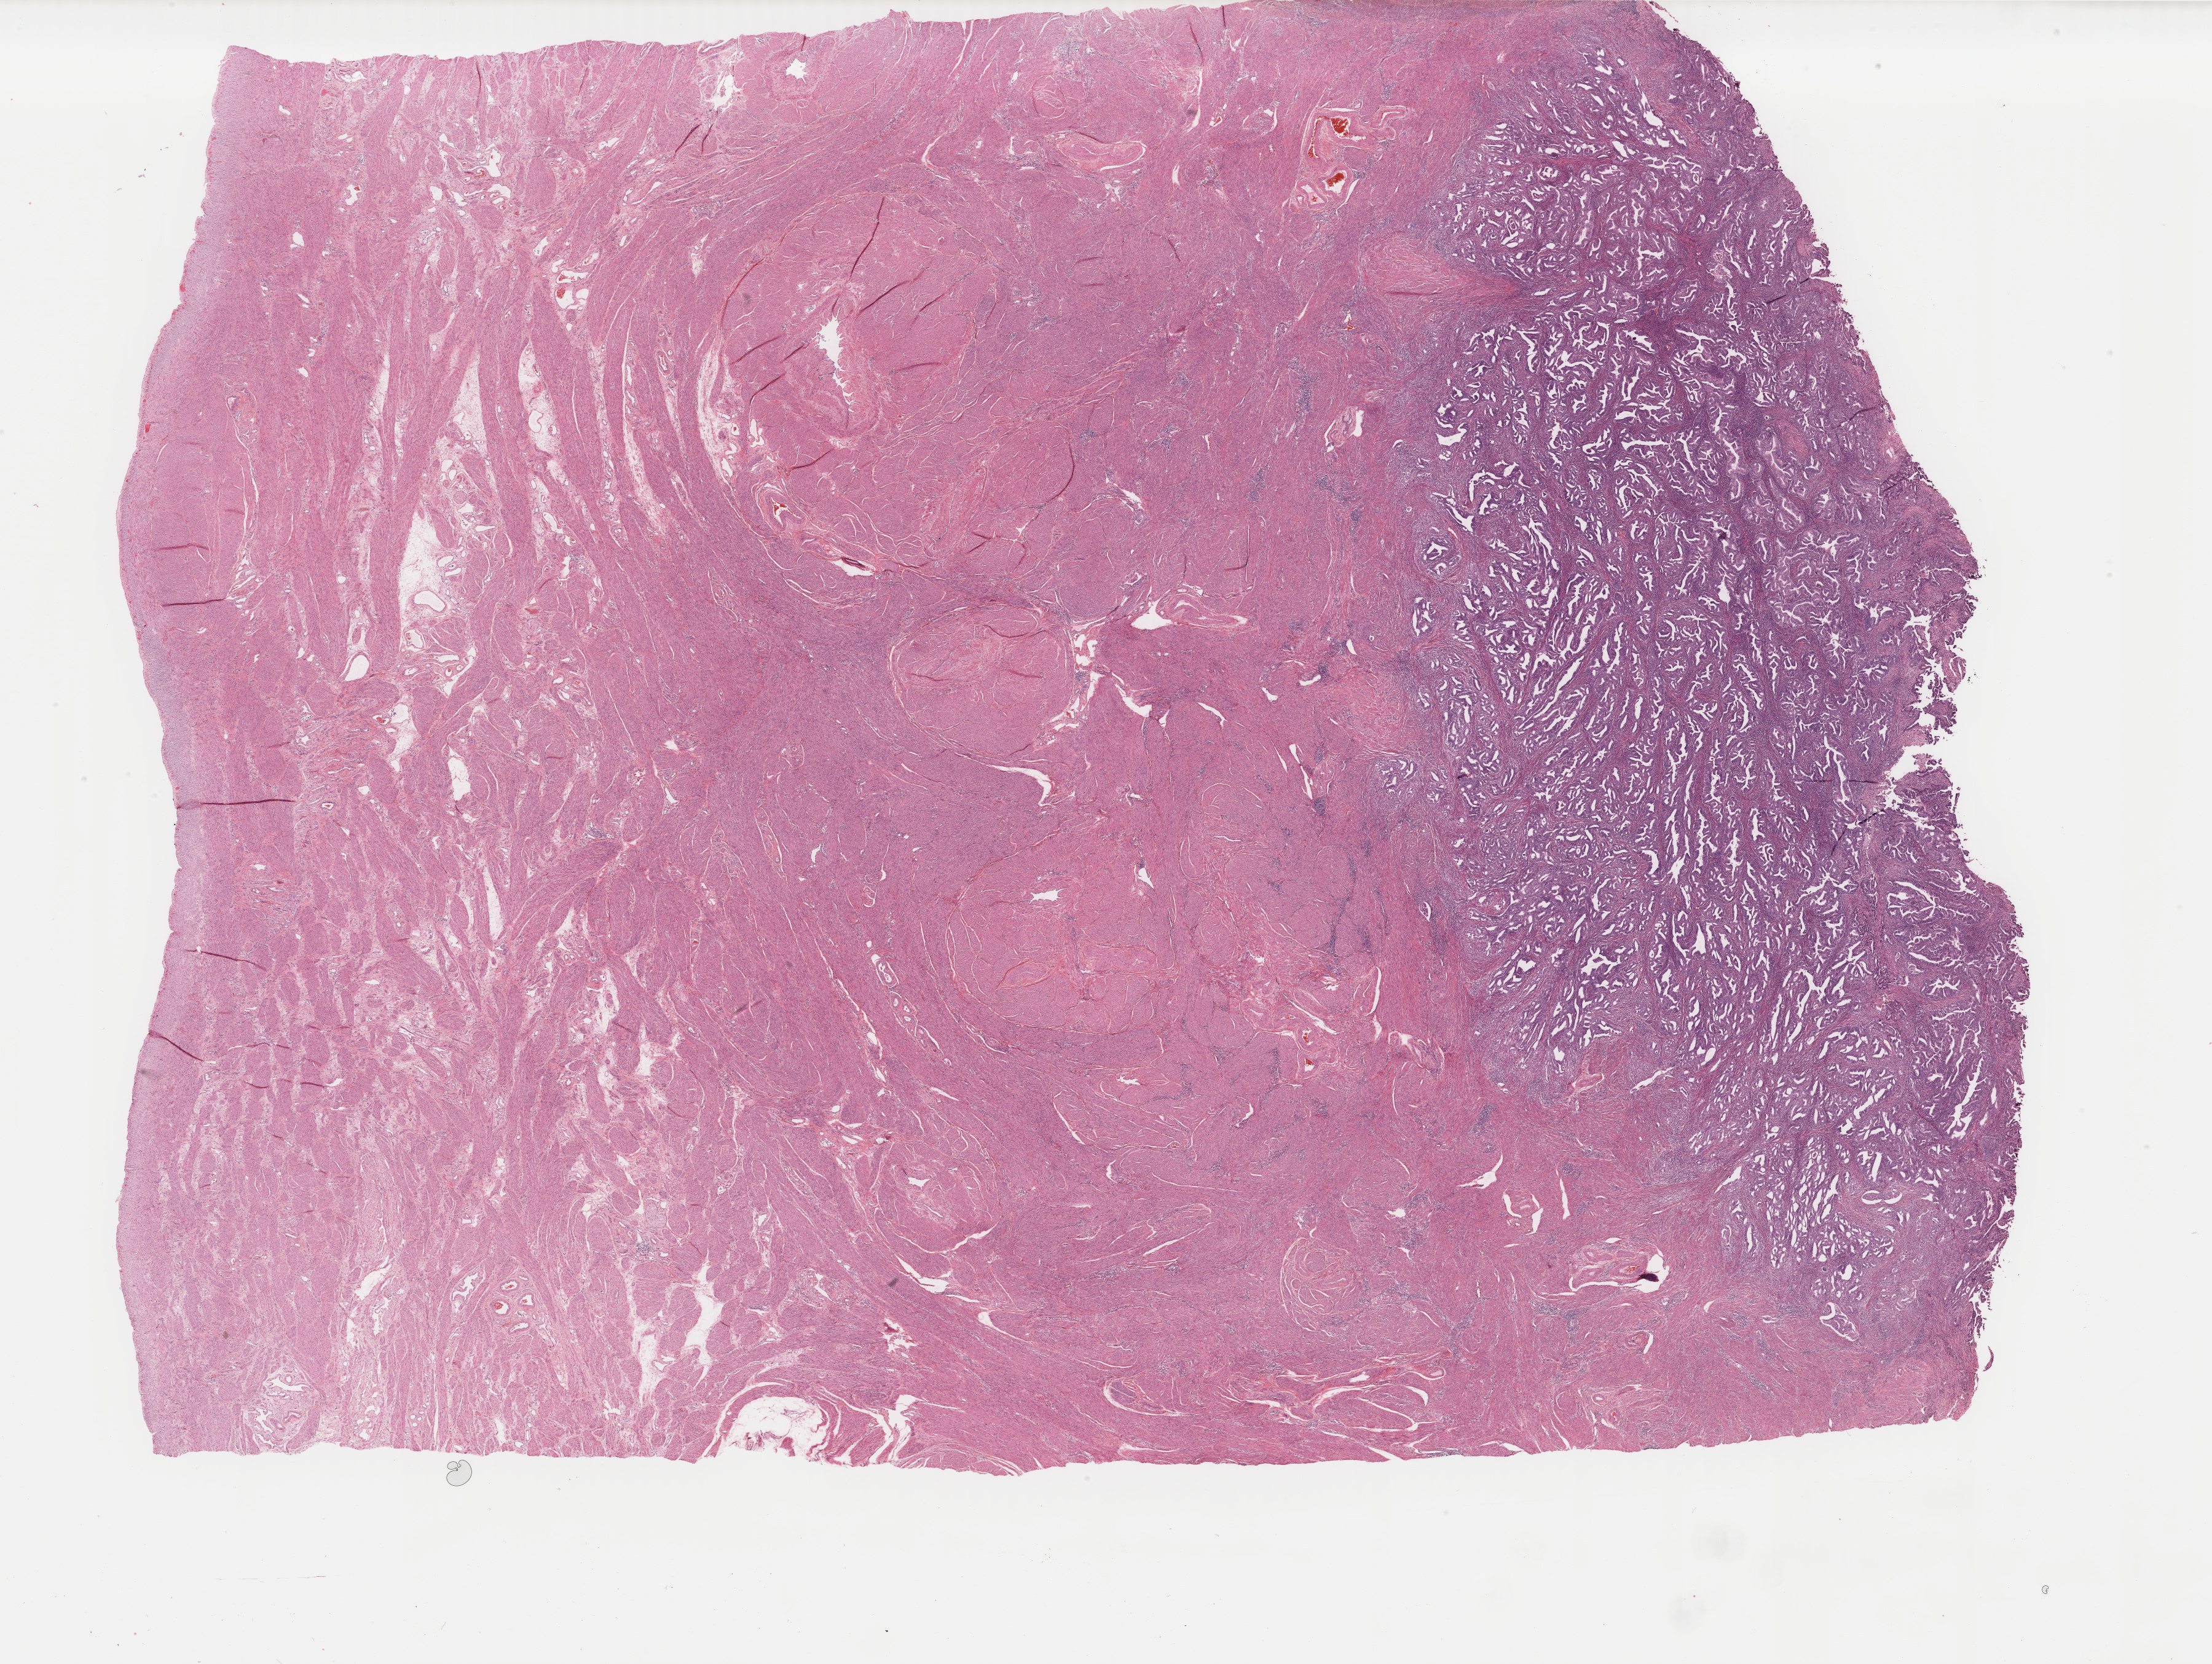
Digitized Hematoxylin and eosin (H&E) stained tissue section (whole slide), shown as a low-resolution overview of the whole scanned area (about 28.6 x 21.5 mm, from a 40x scan); formalin-fixed paraffin-embedded (FFPE) diagnostic section; primary tumour sample from the uterus. Female patient; age at initial diagnosis 53 years. Histologic grade: G3 (poorly differentiated).
Pathologic diagnosis: Endometrioid adenocarcinoma, NOS (endometrium). FIGO stage: IB. Lymph nodes positive (case pathology): 0 of 21 examined.